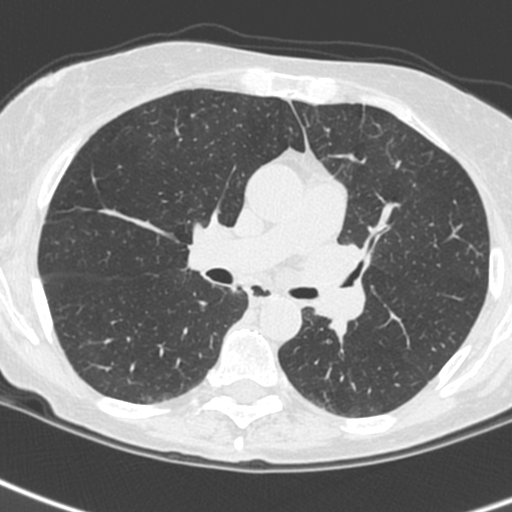
Low-dose screening chest CT, one axial slice. Slice 145 of 242 in the series (ordered by position). 120 kVp. Lung window (W 1500 / L -600 HU). 1.3 mm slice thickness. 512 × 512 image matrix, field of view 284 × 284 mm.
Annotated regions visible in this slice (expert manual segmentation):
- lesion 3 (tumor, upper lobe of left lung): bounding box (x1, y1, x2, y2) in pixels: (299, 240, 367, 328)